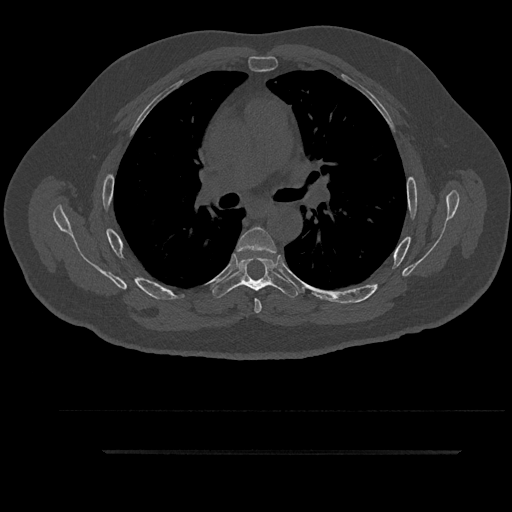
CT including the spine, one axial slice. Position 598 of 797 along the scan axis. Reconstruction kernel Br40s/3. 120 kVp. Bone window (W 1800 / L 400 HU). 512 × 512 image matrix. Male patient, age 63 years. Case-level facts recorded for this patient, not image findings: primary cancer: renal; vertebrae with lytic lesions (as recorded): T8.
Outlined on this slice (semi-automatic segmentation, software-assisted and operator-edited):
- T5 vertebra: bounding box (x1, y1, x2, y2) in pixels: (236, 227, 277, 313)
- T6 vertebra: (211, 256, 299, 298)